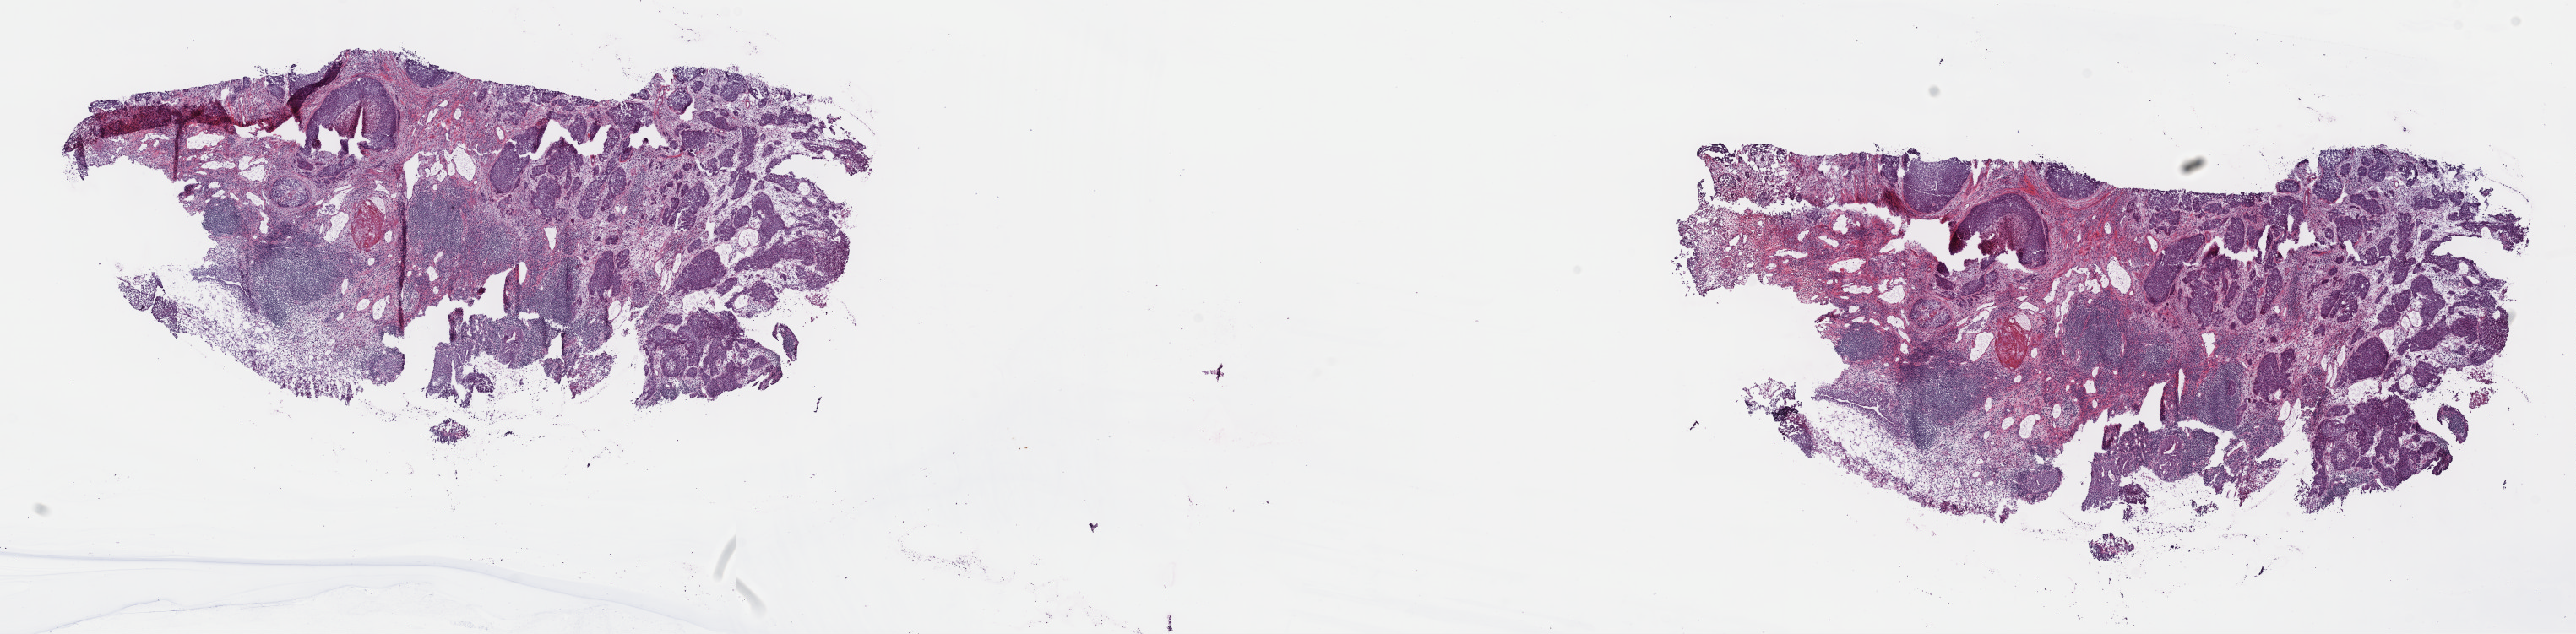
H&E whole-slide image — shown as a low-resolution overview of the whole scanned area (about 24.7 x 6.1 mm). Frozen section from the top of the tissue portion. Primary tumour sample from the bladder. Patient: female, age at initial diagnosis 79 years. Histologic grade: high grade. Slide review estimates, as recorded: tumour cells 97%, tumour nuclei 65%, normal cells 0%, stromal cells 0%, necrosis 3%. Infiltration values recorded for this section: lymphocyte infiltration 7%, monocyte infiltration 0%, neutrophil infiltration 0%.
Pathologic diagnosis: Transitional cell carcinoma (posterior wall of bladder). TNM: T4a N0 MX. AJCC pathologic stage: III (7th edition).